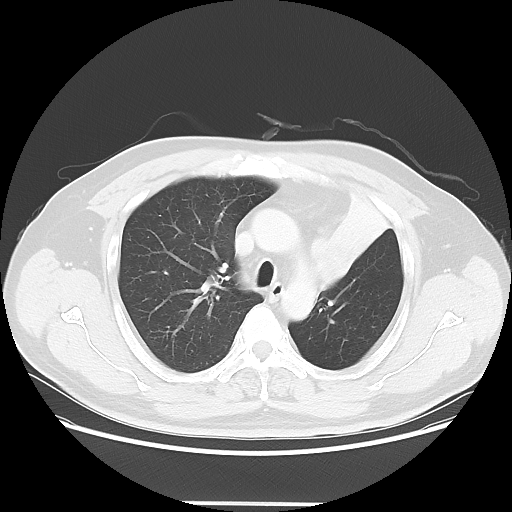
Chest CT, one axial slice. Reconstruction kernel LUNG. 120 kVp. Lung window (W 1500 / L -600 HU). 5 mm slice thickness. 512 × 512 image matrix, field of view 403 × 403 mm. Male patient, age 49 years. Case-level facts recorded for this patient, not image findings: clinical TNM (as recorded): T3 N3 M1c.
Annotated regions visible in this slice (rectangle marked by the reading radiologist):
- lung tumour (recorded histology: squamous cell carcinoma): box from (x=304, y=229) to (x=356, y=299) px